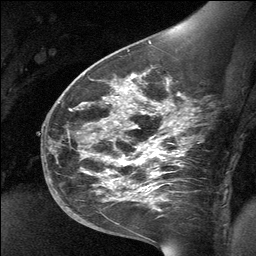
Breast MRI (dynamic contrast-enhanced), one sagittal slice; slice 40 of 64 in the series (ordered by position); dynamic contrast-enhanced study with each time point stored as its own series, time point 2 of 3 at this slice position (early post-contrast, ordered by acquisition time); 1.5 T; TE 4.8 ms, TR 27 ms; 256 × 256 image matrix, field of view 200 × 200 mm. Female patient, age 39 years. Case-level facts recorded for this patient, not image findings: setting: breast cancer imaged before/during neoadjuvant chemotherapy; receptor status: HER2-positive.
Annotated regions visible in this slice (semi-automatically segmented with operator editing):
- analysis volume of interest (the breast-tissue region the enhancement analysis was run in; not a lesion): bounding box [x1, y1, x2, y2] px = [70, 69, 197, 224]
- tumour enhancement mask (voxels above the 90 % enhancement threshold inside the analysis volume of interest): [107, 75, 160, 191]